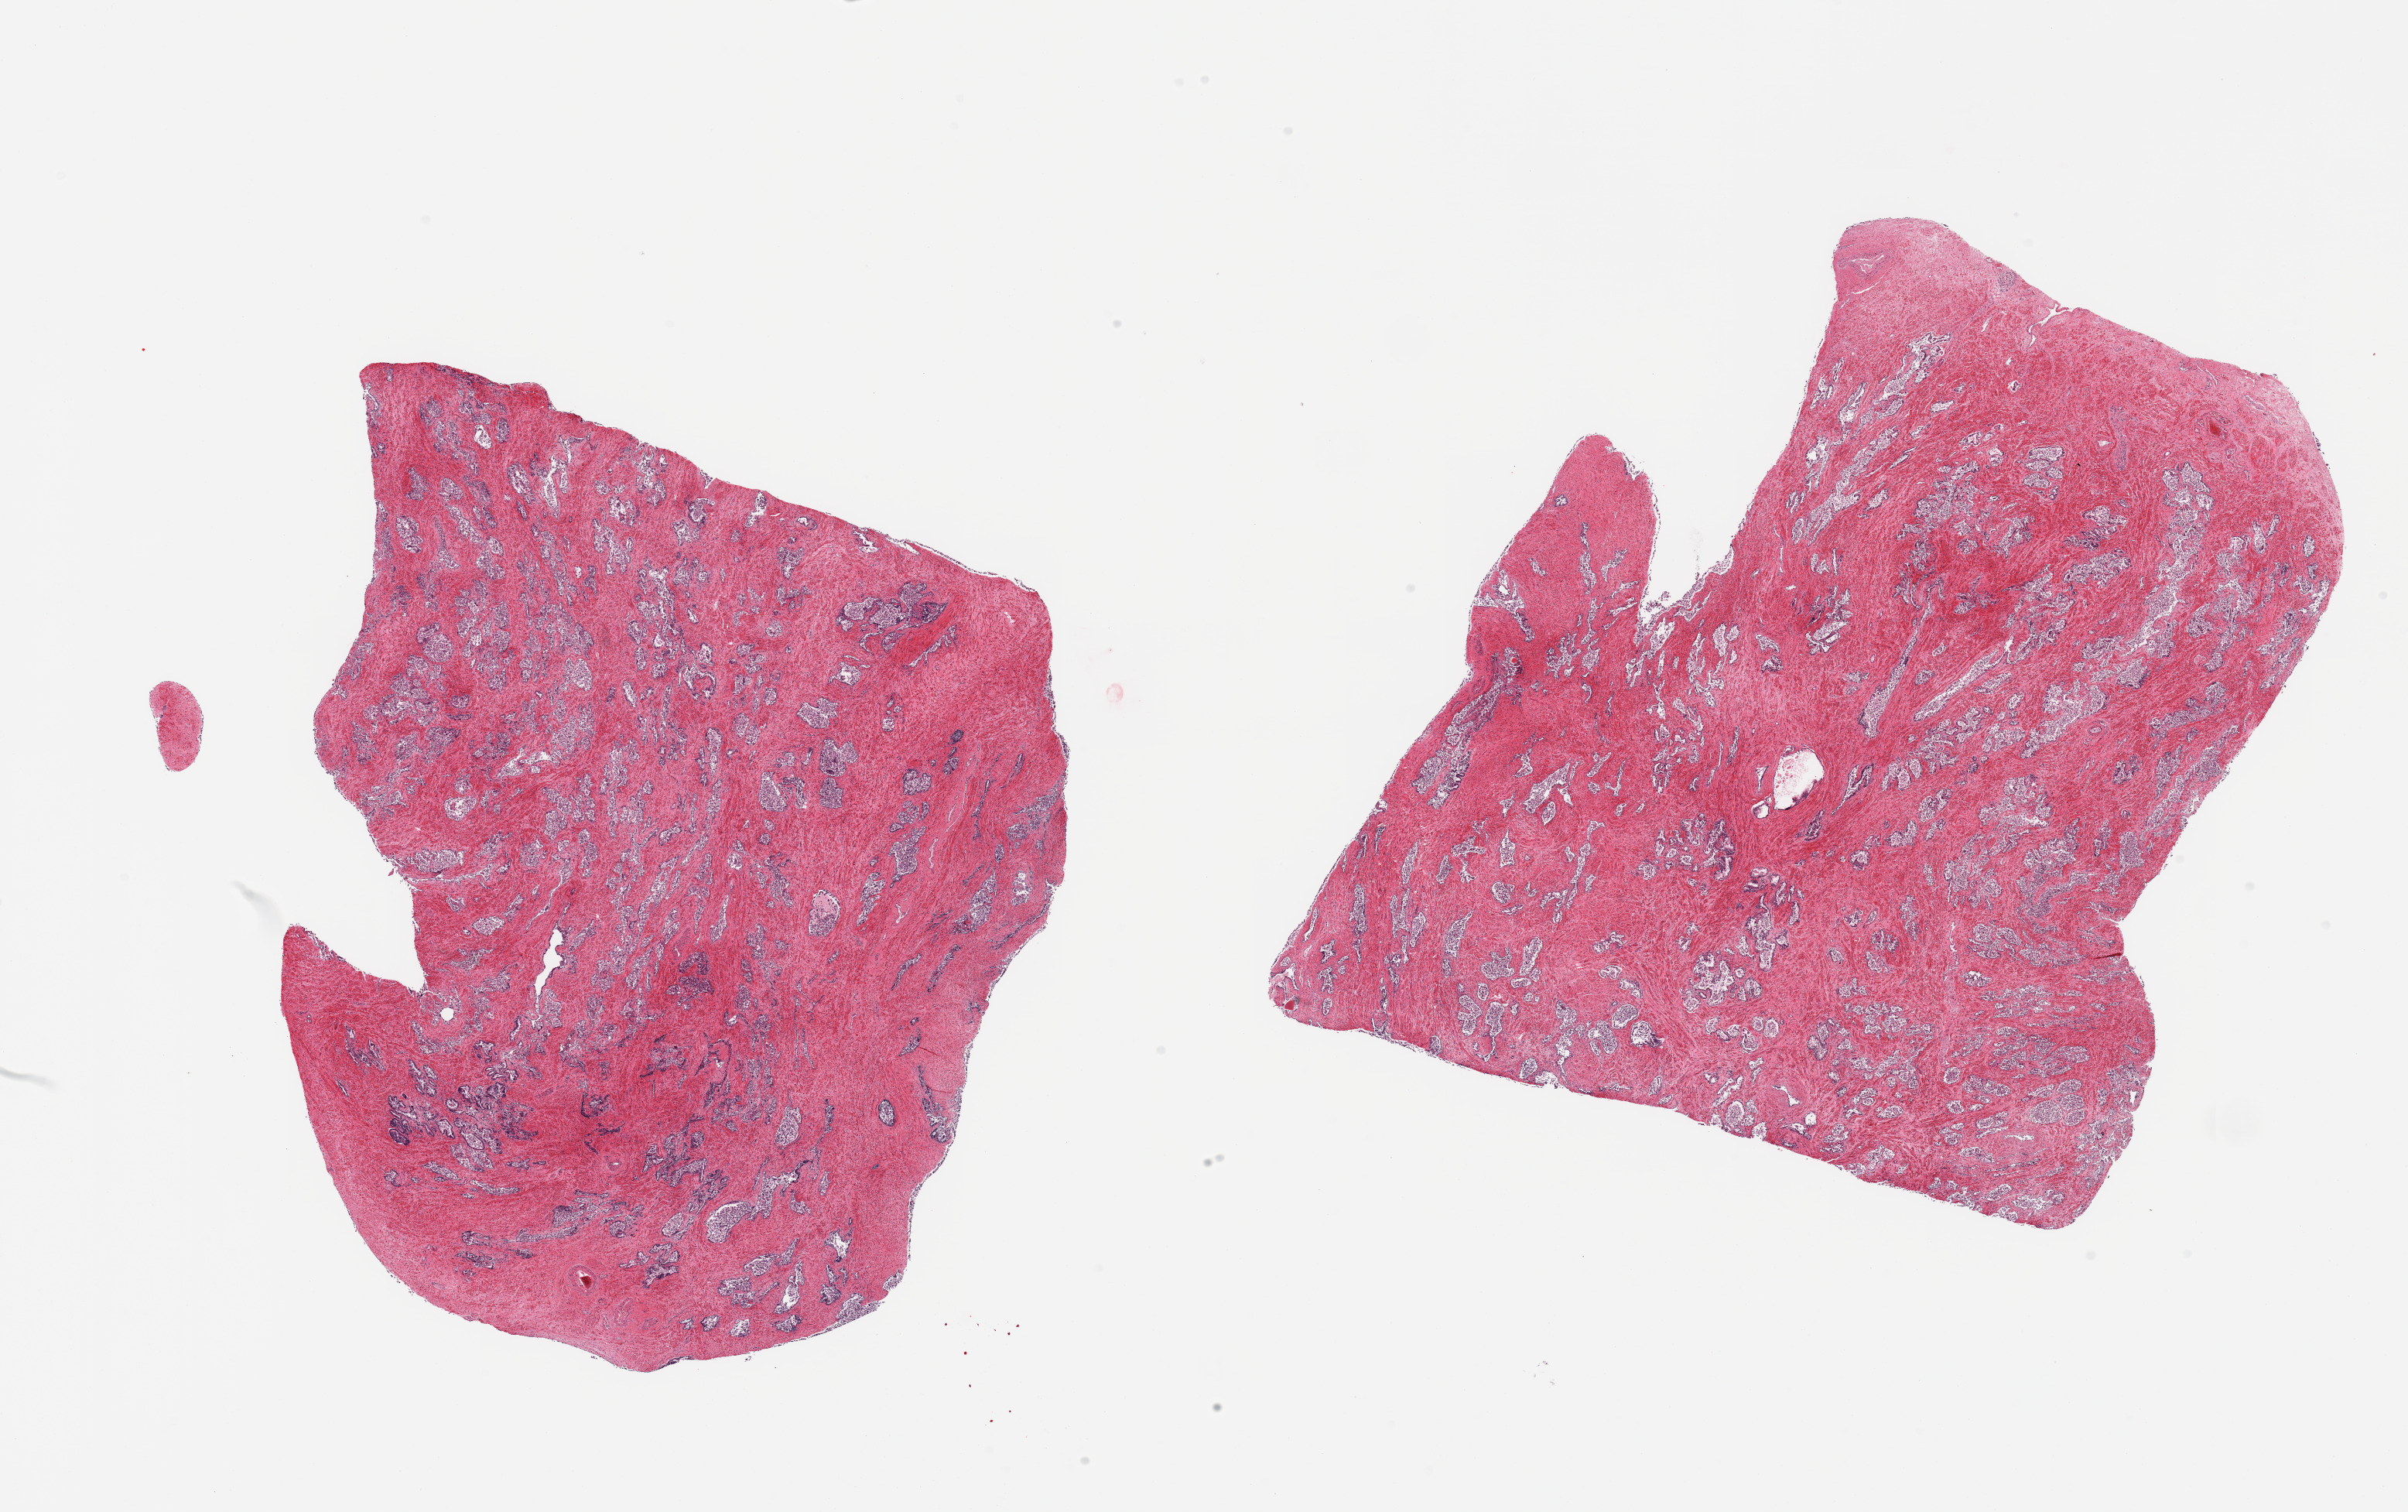
Whole-slide image, haematoxylin and eosin stain — whole scanned area (about 24.6 x 15.5 mm) shown as a low-resolution overview, PAXgene-fixed, paraffin-embedded tissue, sampled site (target tissue): prostate, donor tissue sample. Donor sex: male.
Pathologist's review note for this sample: 2 pieces; fibromuscular stroma with glands with predominantly sloughed epithelium.